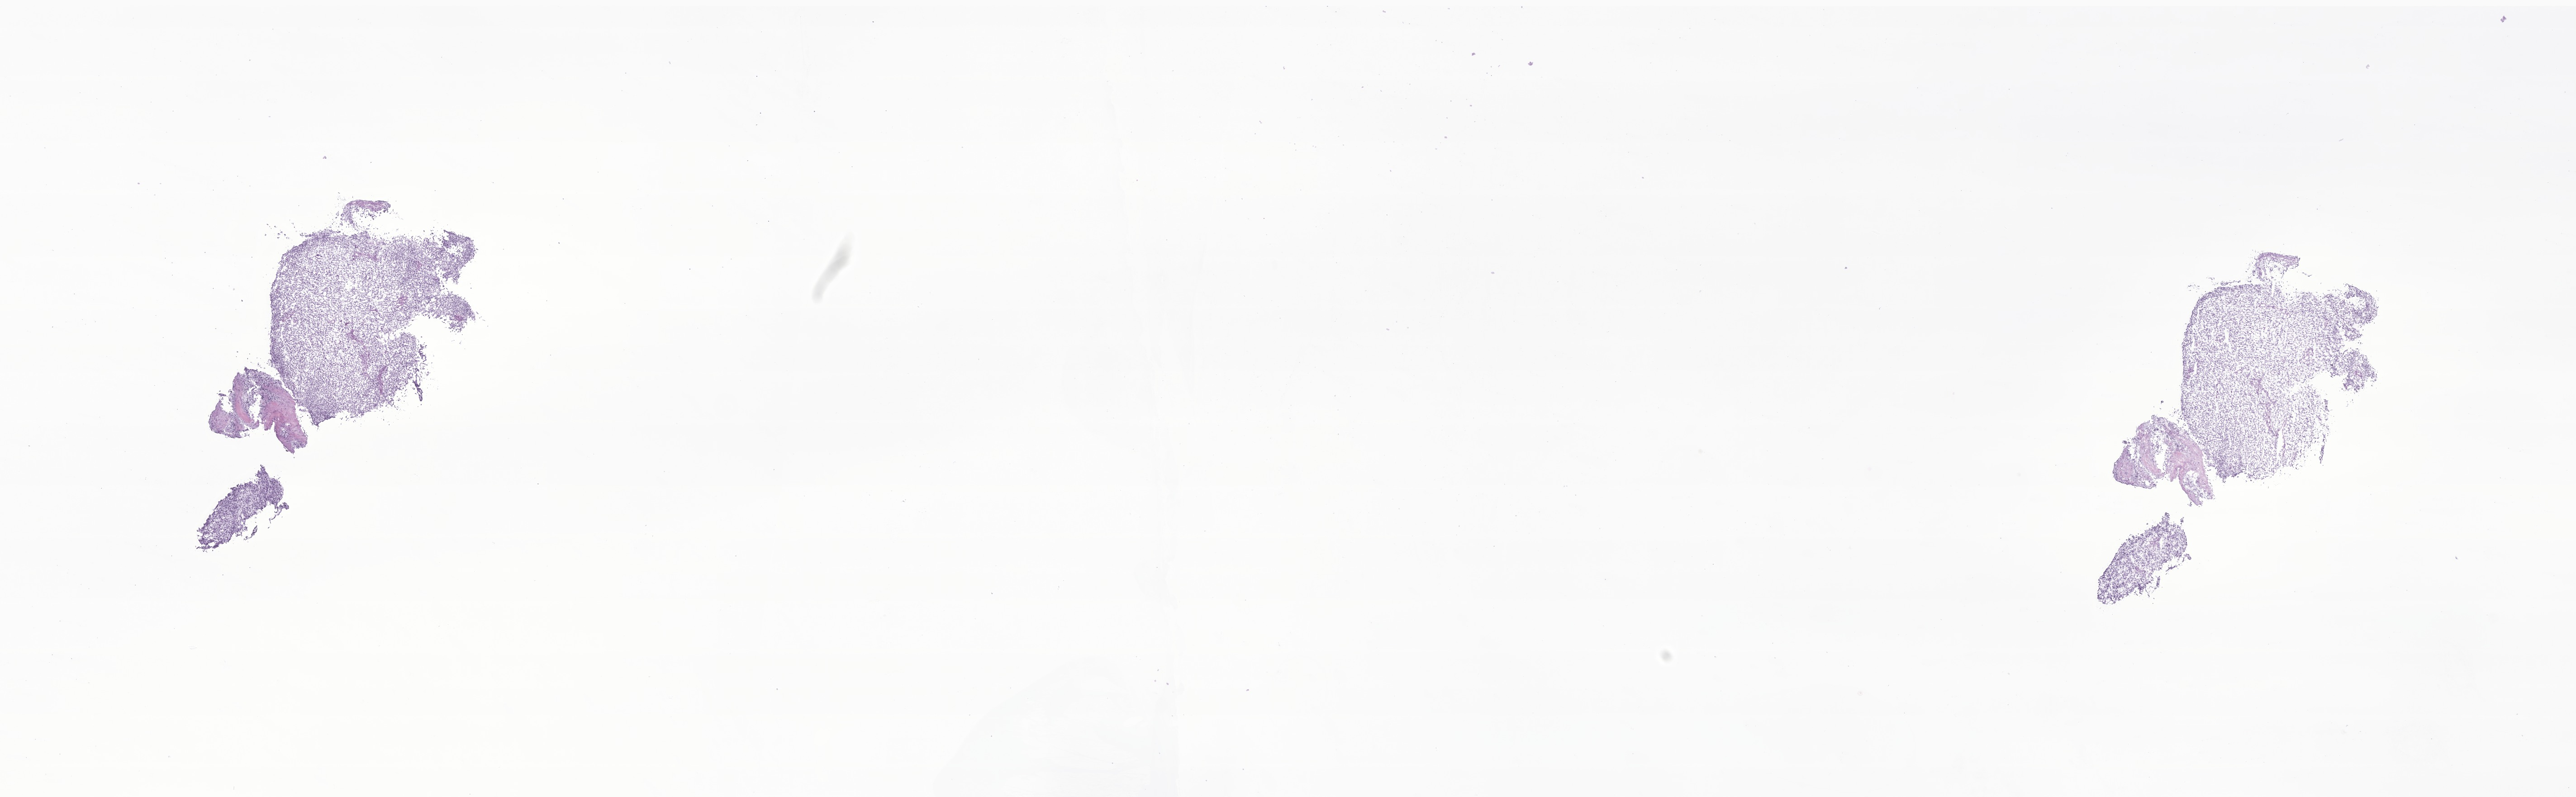
Whole-slide image, haematoxylin and eosin stain of tumor tissue from the pelvis, a low-resolution overview of the entire scanned area, about 24.0 x 7.4 mm. Frozen section (OCT-embedded). Female patient, age 111 months (9 years 3 months).
Recorded diagnosis: Rhabdomyosarcoma, NOS.